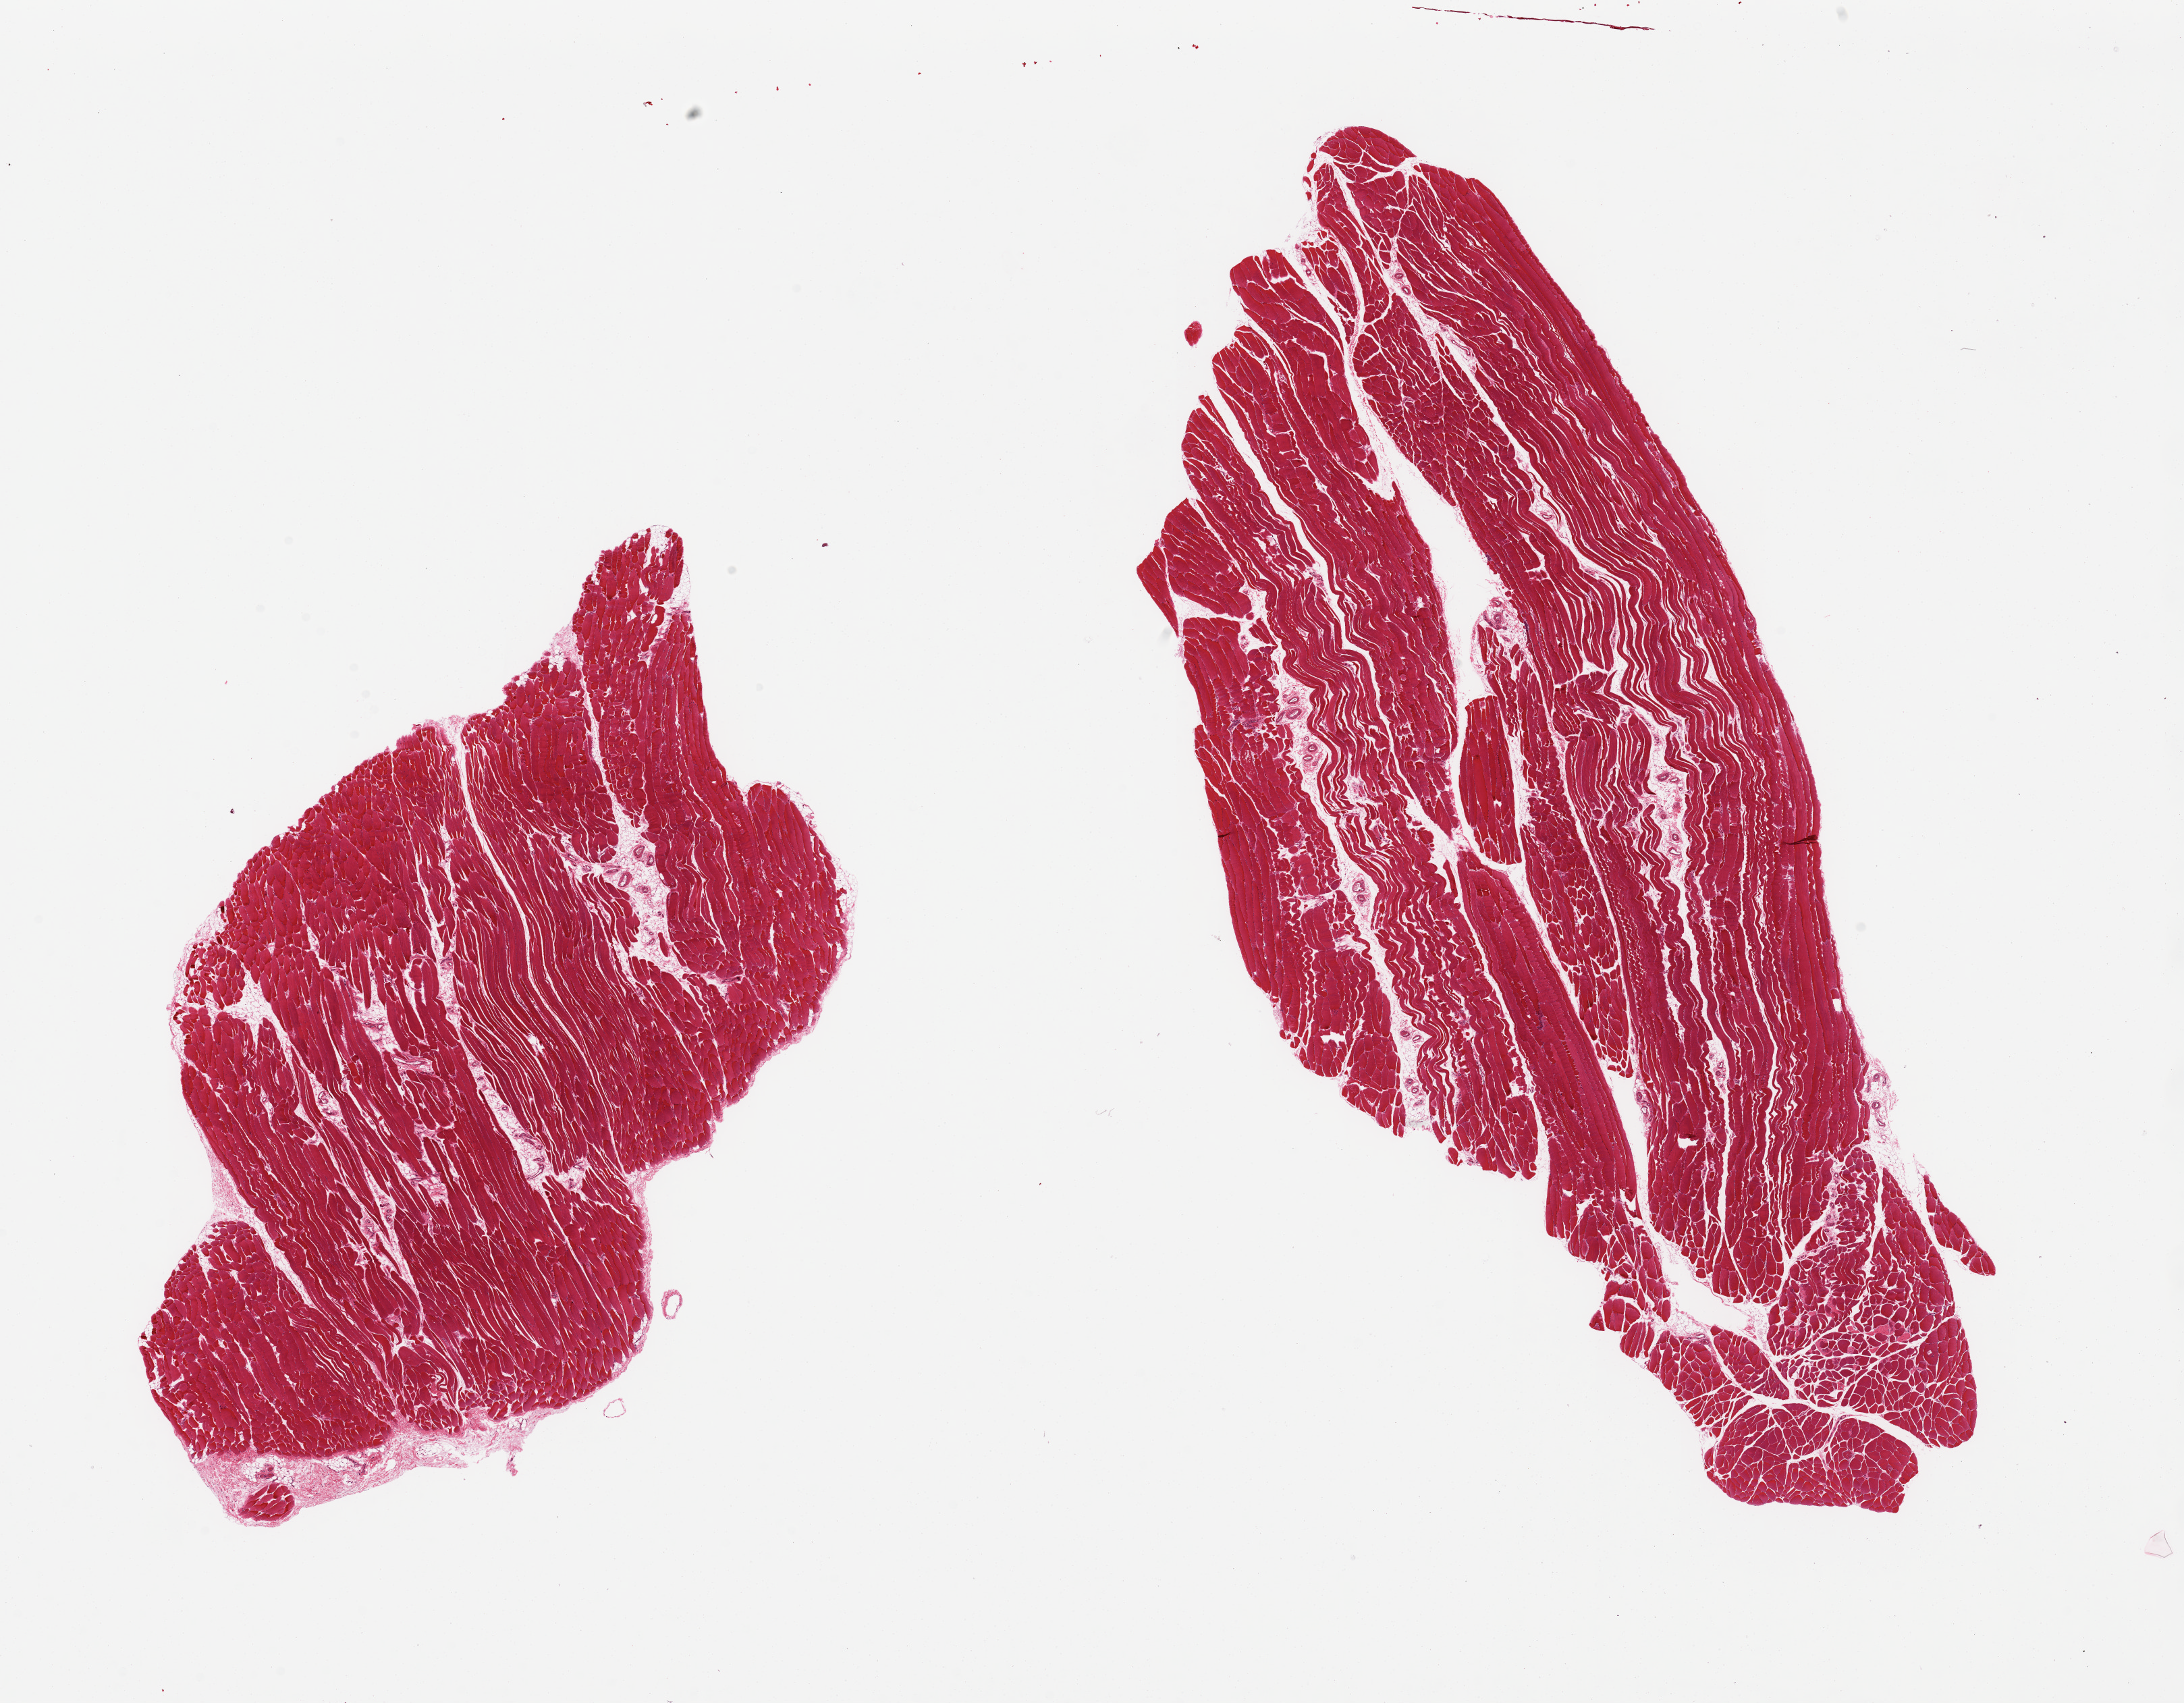
H&E whole-slide image — shown as a low-resolution overview of the whole scanned area (about 25.6 x 20.0 mm), PAXgene-fixed, paraffin-embedded tissue, sampled site (target tissue): skeletal muscle, donor tissue sample.
• reviewer comment on this tissue sample: 2 pieces, minimal interstitial fat